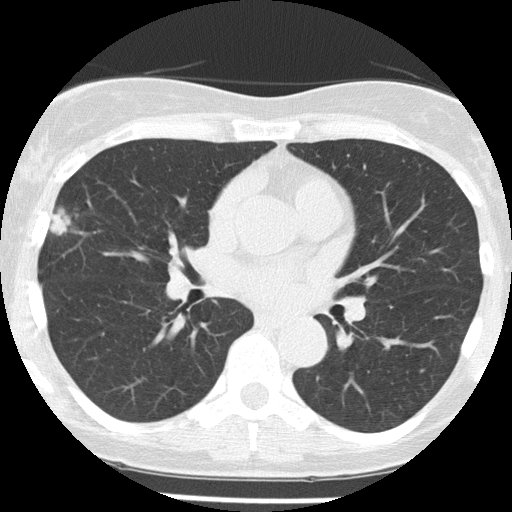
Low-dose screening chest CT, one axial slice. Position 85 of 156 along the scan axis. Reconstruction kernel FC51. Lung window (W 1500 / L -600 HU). 2 mm slice thickness. 512 × 512 image matrix, field of view 280 × 280 mm.
Structures marked on this image (expert manual segmentation):
- lesion 1 (tumor, middle lobe of right lung): bounding box (x1, y1, x2, y2) in pixels: (50, 208, 71, 236)